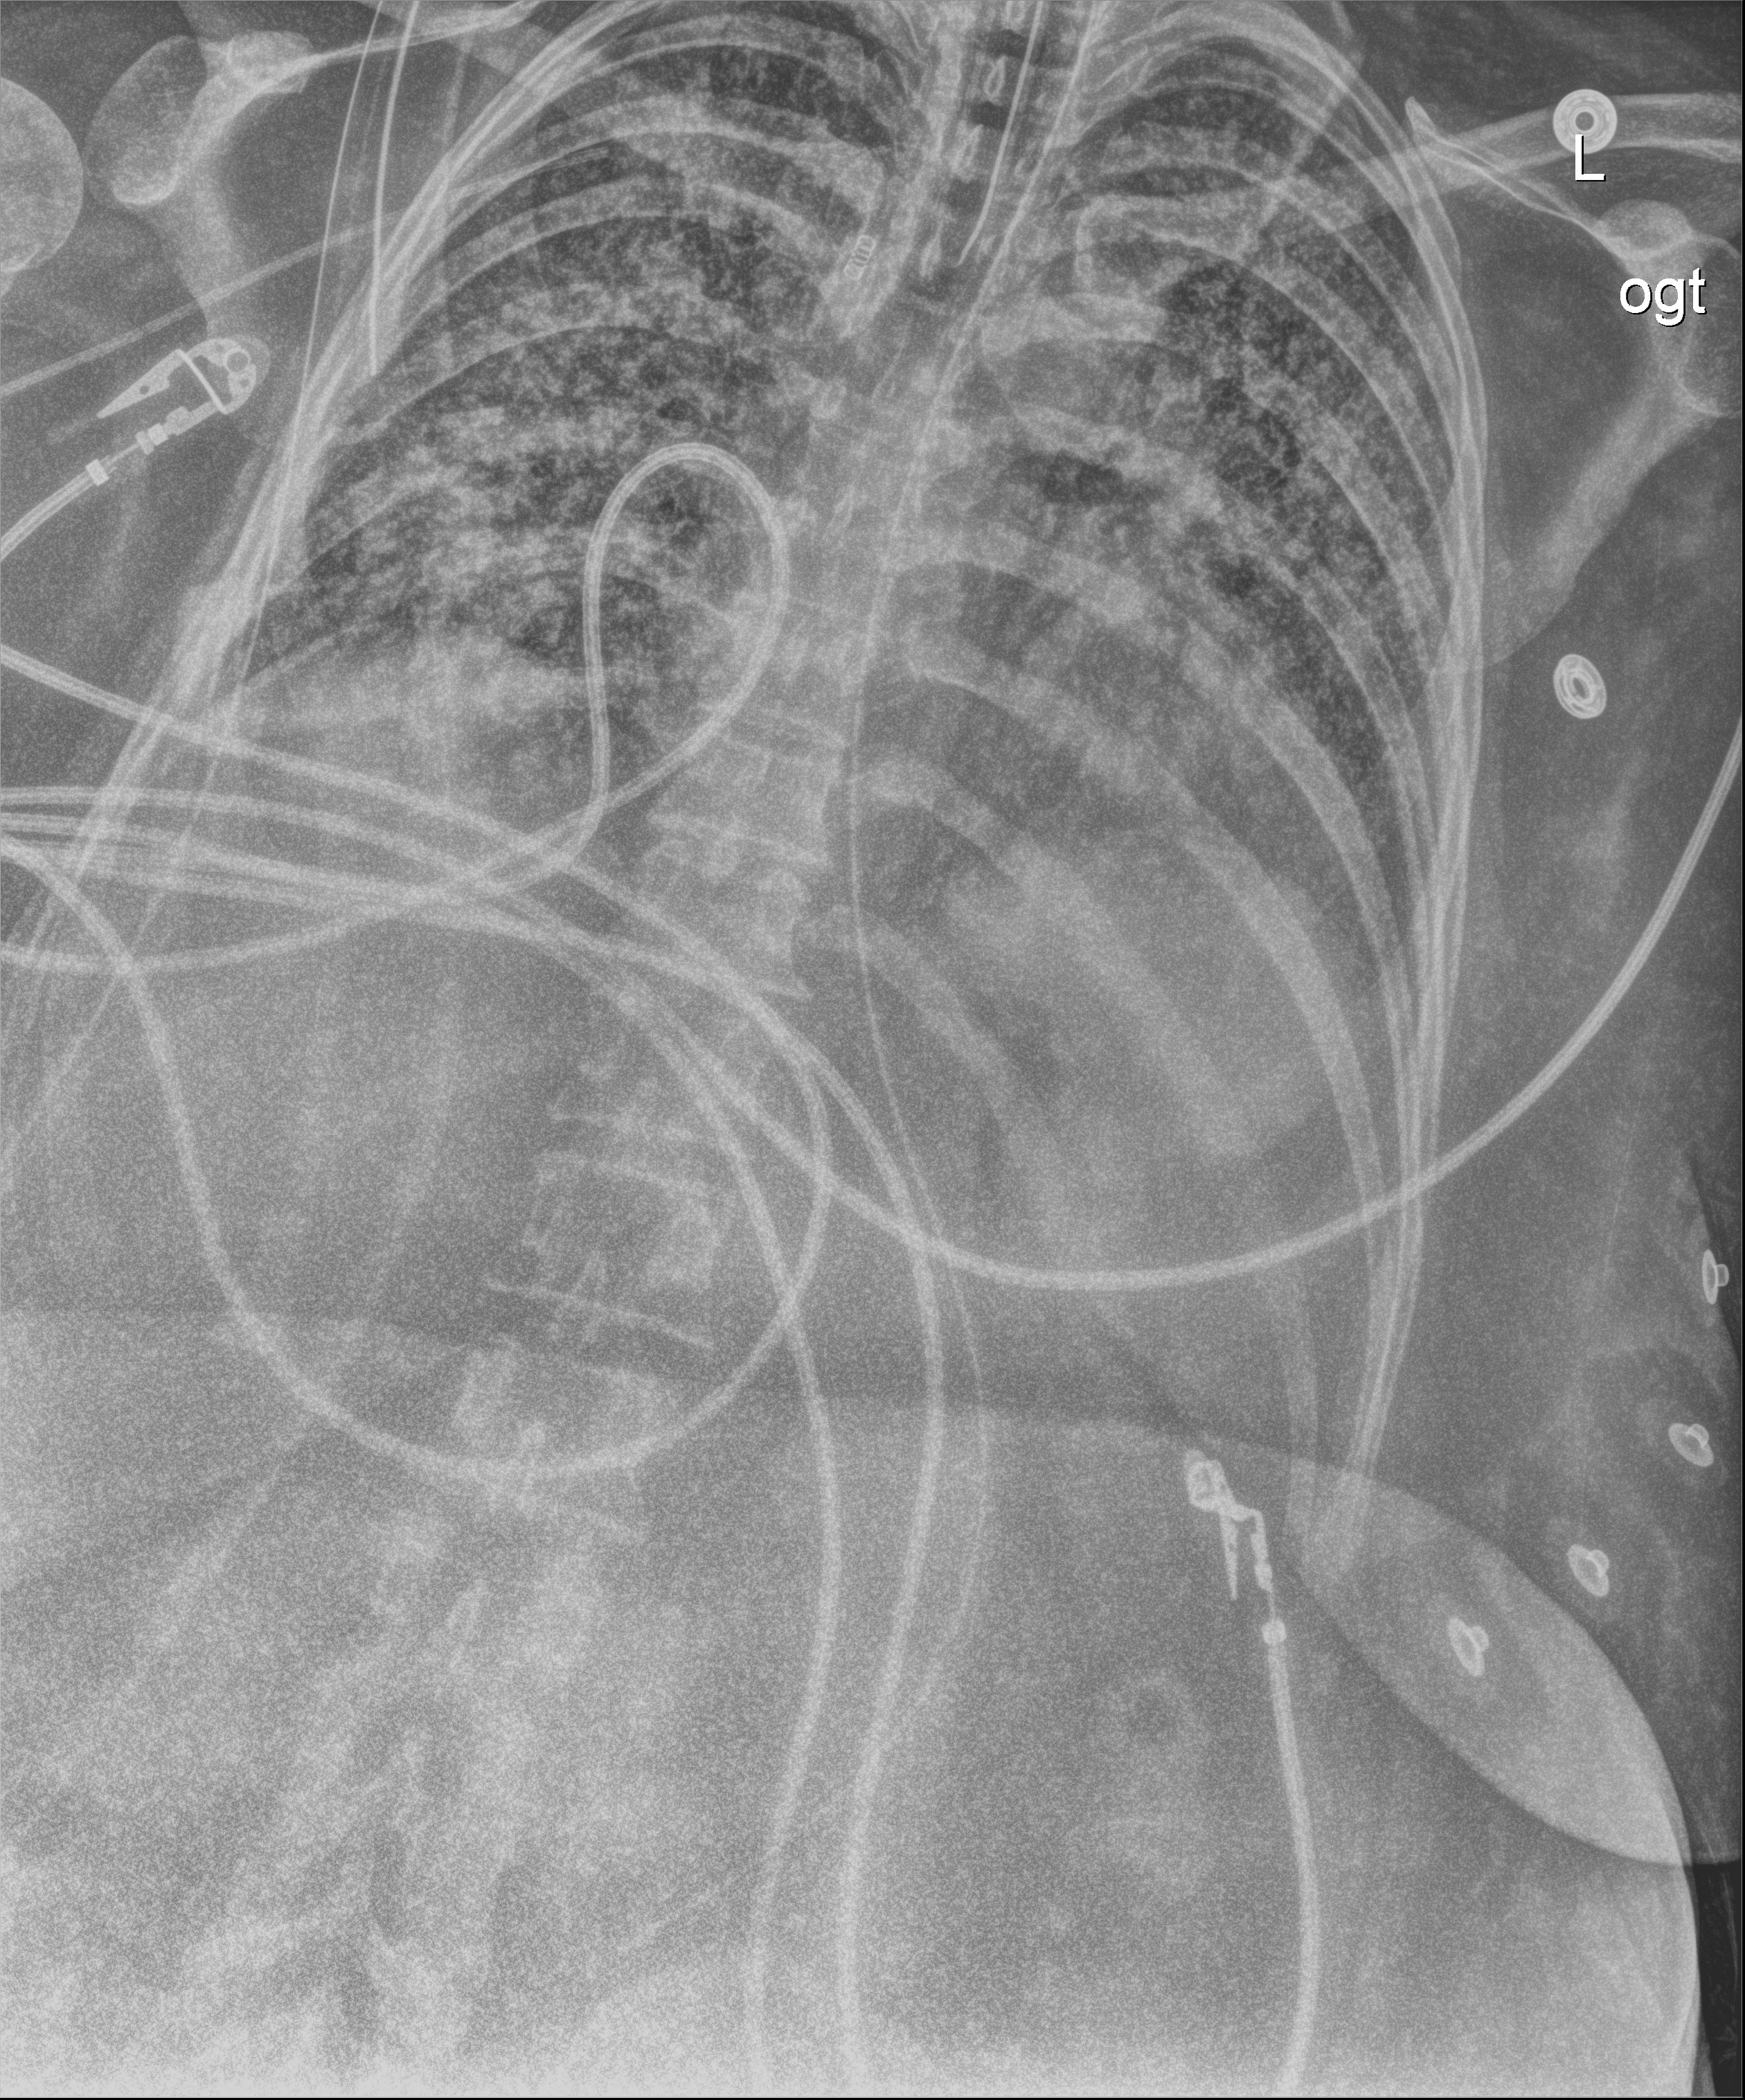
Portable chest radiograph. Patient hospitalised with COVID-19; female, aged 18–59 years.
Hospital-stay facts (about this admission, not read from this image; timing relative to this image not recorded):
- other chronic lung disease (admission record): no